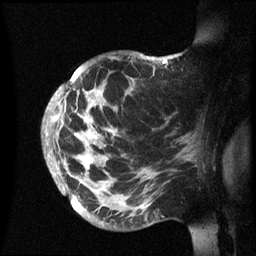
Breast MRI (dynamic contrast-enhanced), one sagittal slice; position 43 of 60 along the scan axis; dynamic contrast-enhanced series, image 2 of 3 at this slice position (ordered by acquisition); 1.5 T; TE 4.2 ms, TR 8.4 ms; 2.4 mm slice thickness; 256 × 256 image matrix. Patient: female, 48 years.
Annotated regions visible in this slice (semi-automatically segmented with operator editing):
- analysis volume of interest (the breast-tissue region the enhancement analysis was run in; not a lesion): box from (x=43, y=54) to (x=202, y=236) px
- tumour enhancement mask (voxels above the 70 % enhancement threshold inside the analysis volume of interest): (x=46, y=56)–(x=173, y=193)